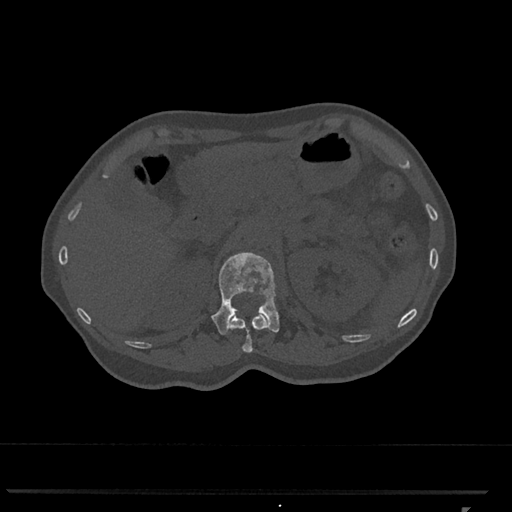
CT including the spine, one axial slice. Position 424 of 793 along the scan axis. Reconstruction kernel Br40s/3. 120 kVp. Bone window (W 1800 / L 400 HU). 0.5 mm slice thickness. 512 × 512 image matrix. Female patient, age 62 years. From the clinical record (not read from this slice): primary cancer: renal.
Annotated regions visible in this slice (semi-automatically segmented with operator editing):
- L1 vertebra: bounding box <211,252,279,335> (left, top, right, bottom; pixels)
- T12 vertebra: <229,312,267,353>